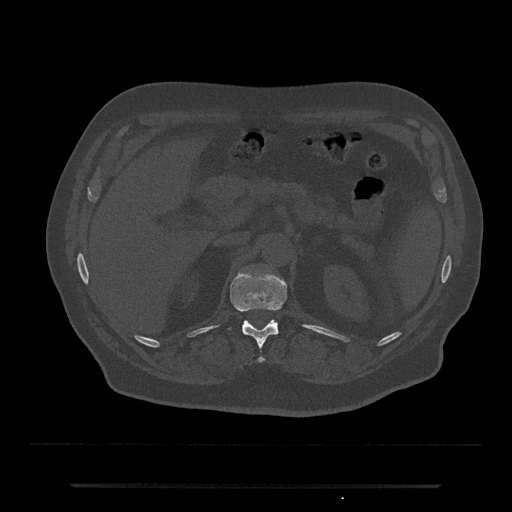
CT including the spine, one axial slice. Position 585 of 797 along the scan axis. Reconstruction kernel Br40s/3. 120 kVp. Bone window (W 1800 / L 400 HU). 512 × 512 image matrix. Patient: male, 80 years. Case-level facts recorded for this patient, not image findings: primary cancer: prostate.
Outlined on this slice (semi-automatic segmentation, software-assisted and operator-edited):
- T12 vertebra: bounding box [x1, y1, x2, y2] px = [229, 273, 287, 363]